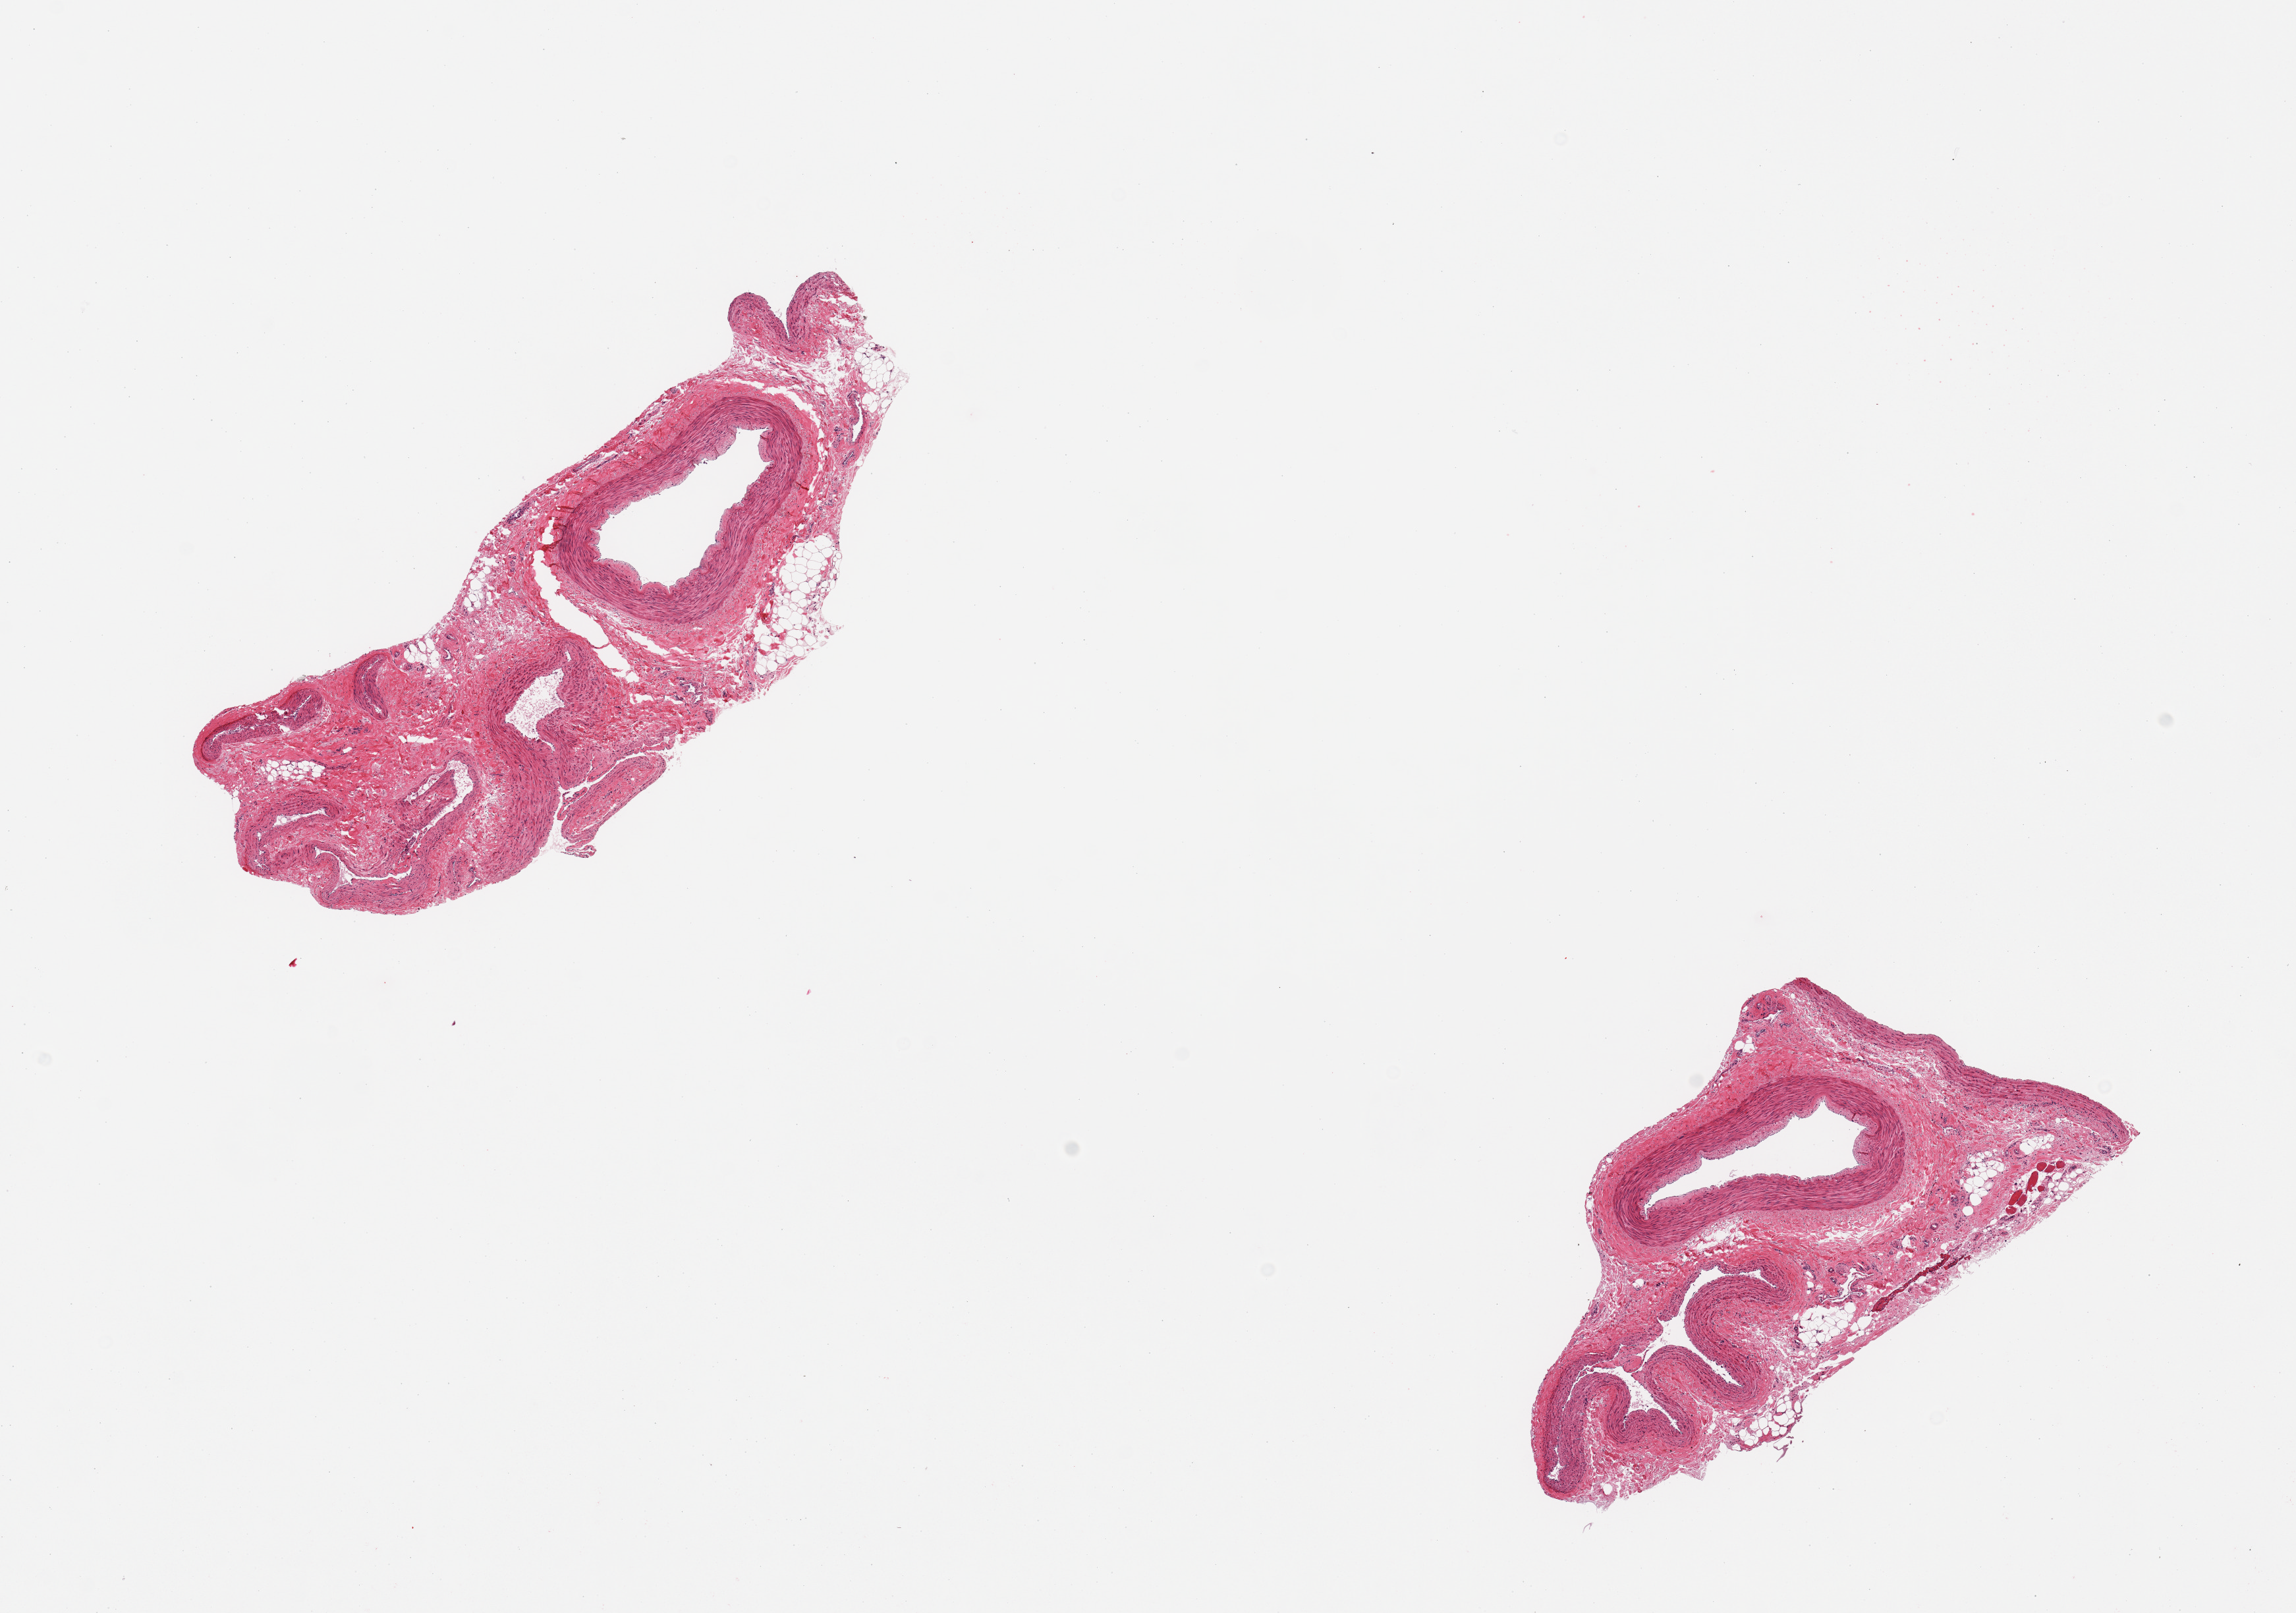
Whole-slide image, hematoxylin and eosin (H&E) stain — shown as a low-resolution overview of the whole scanned area (about 13.8 x 9.7 mm); PAXgene-fixed, paraffin-embedded tissue; section of tibial artery (target tissue); donor tissue sample. Donor sex: female.
Reviewer comment on this tissue sample: 2 pieces; ~50--70% is associated adventitia with venous component.